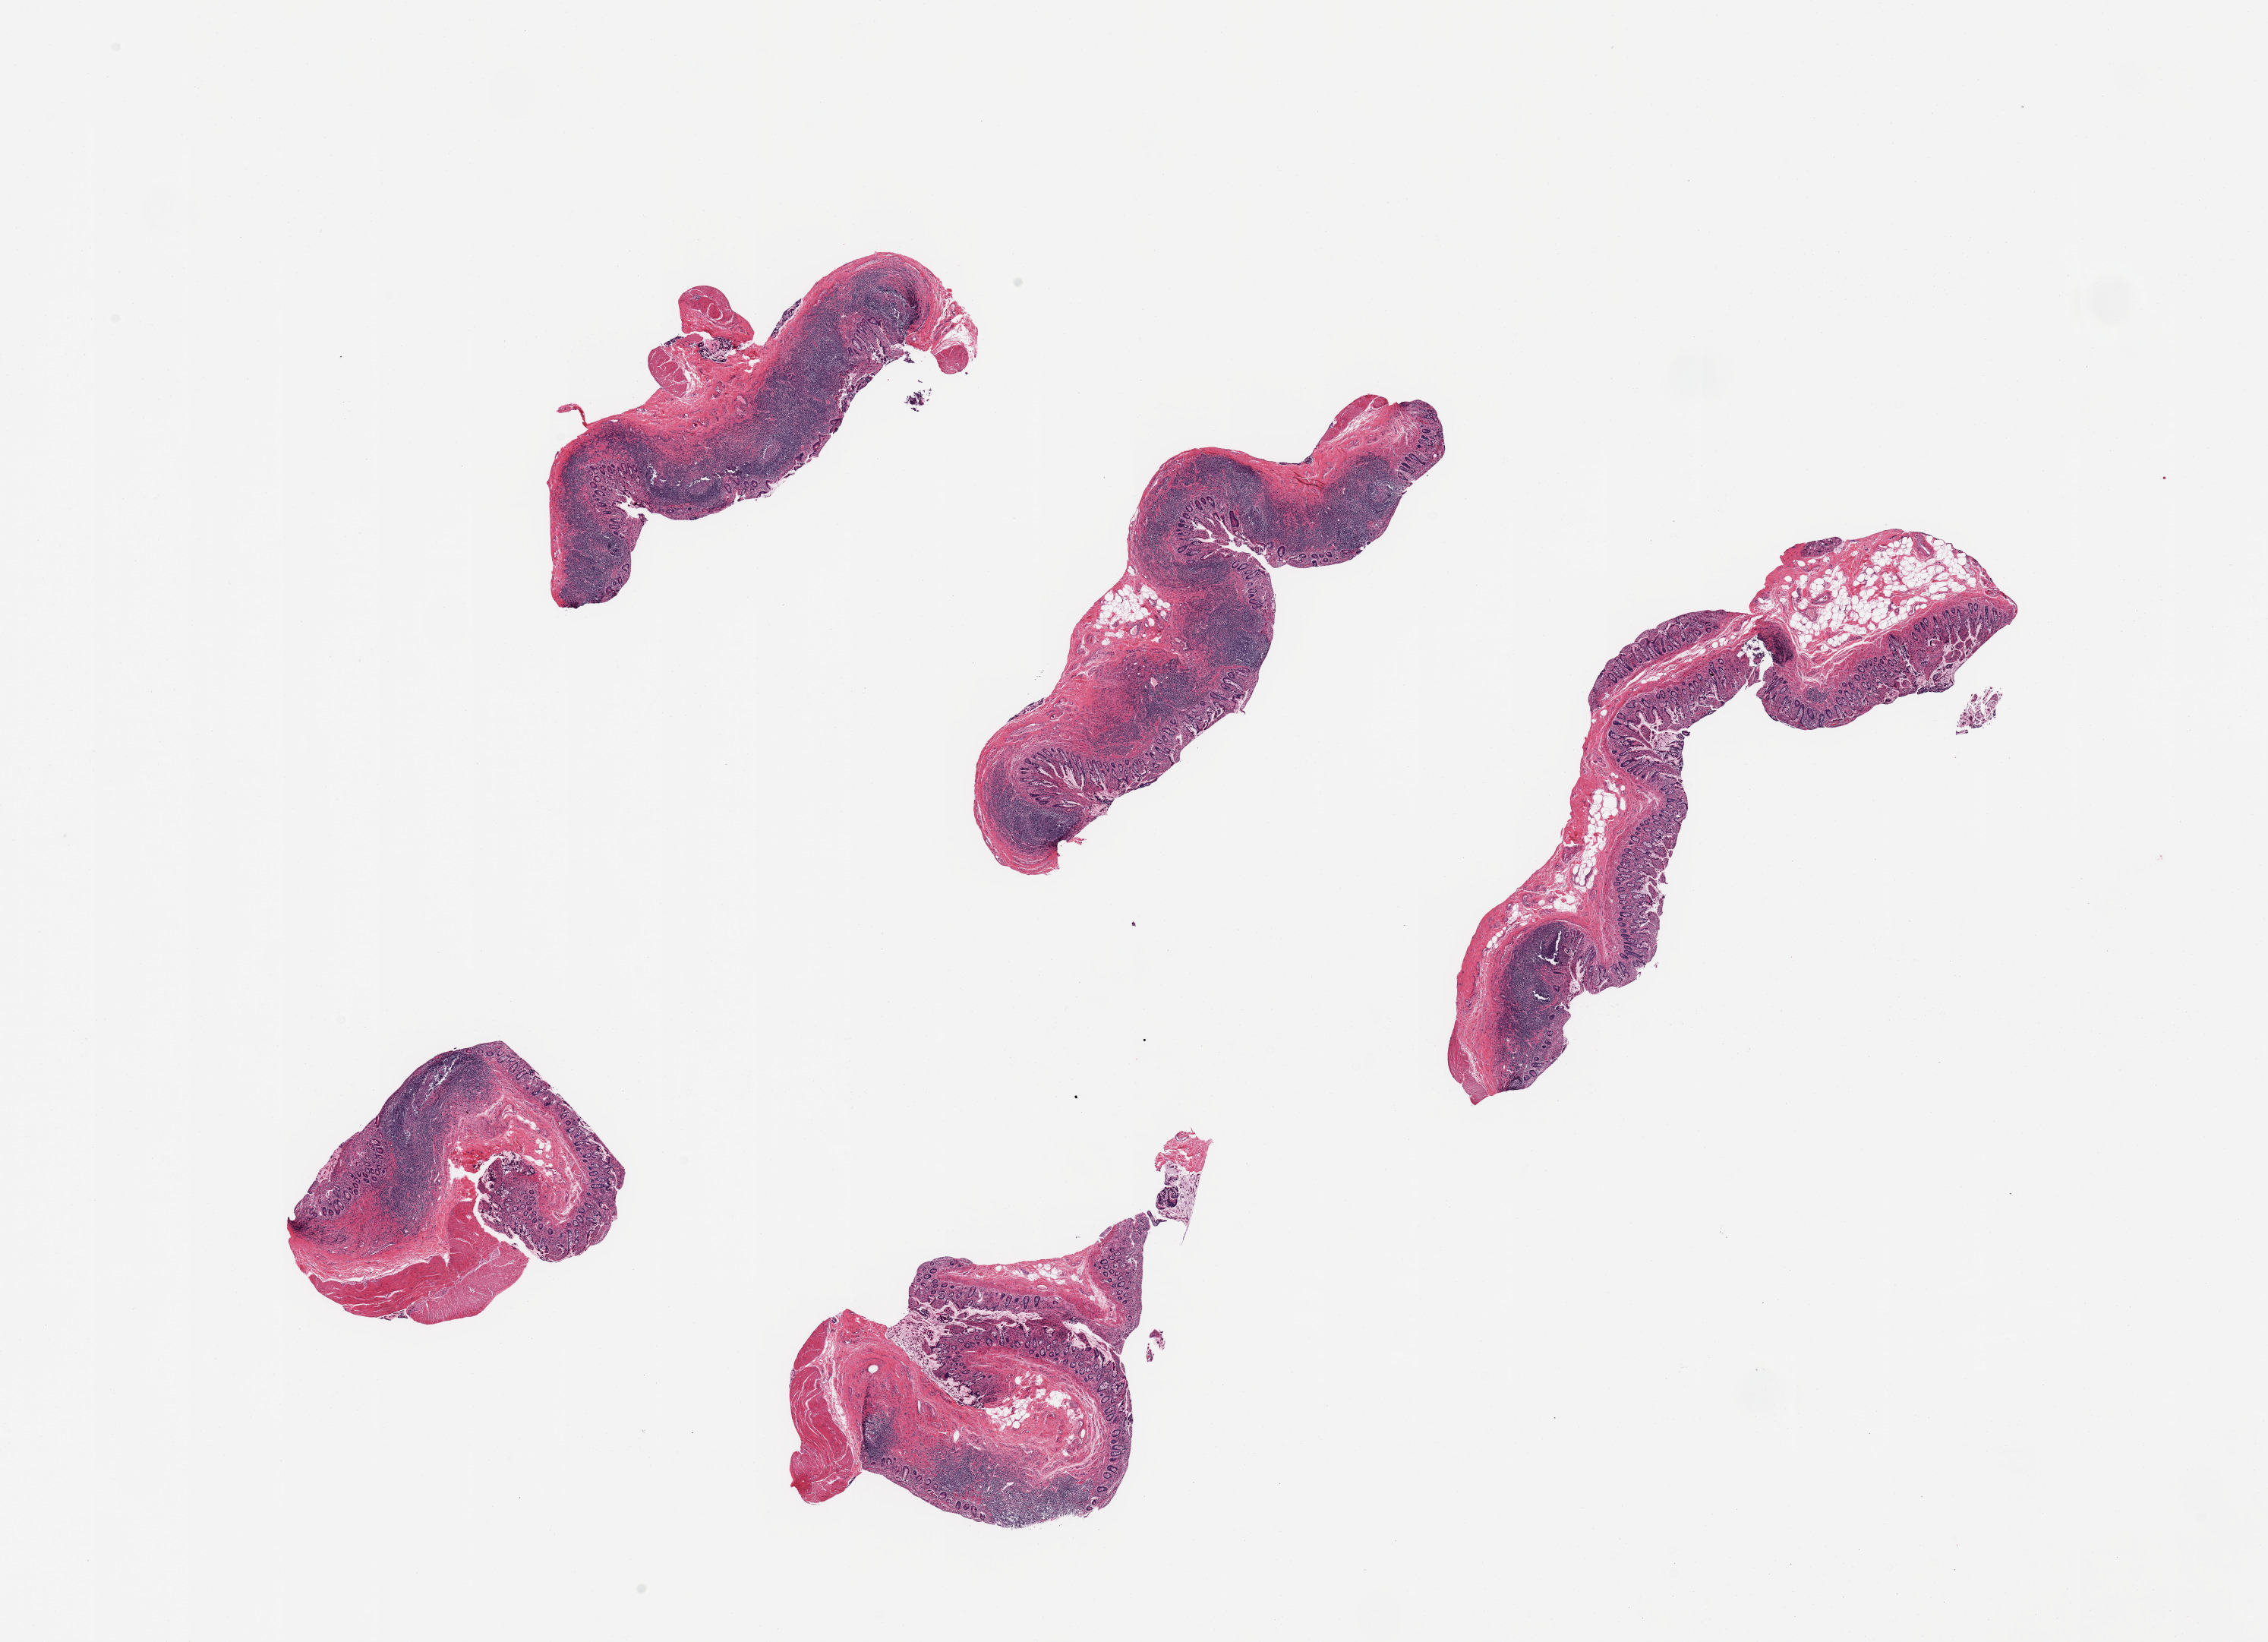
Whole-slide image, haematoxylin and eosin stain, brightfield, low-resolution overview of the scanned area, about 23.6 x 17.1 mm (from a 20x scan). PAXgene-fixed paraffin-embedded (PFPE) section. Sampled site (target tissue): ileum. Donor tissue sample. Donor sex: male.
Review note (as recorded): 5 pieces; abundant lymphoid nodules in 4 pieces; well dissected.